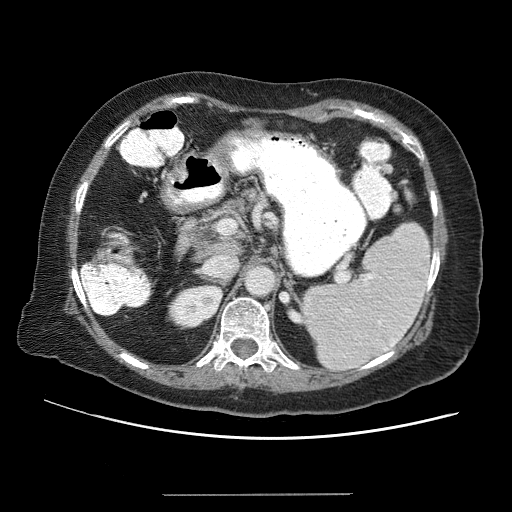
Contrast-enhanced abdominal CT (liver protocol), one axial slice; slice 28 of 65 in the series (ordered by position); reconstruction kernel STANDARD; soft-tissue window (W 400 / L 40 HU); 512 × 512 image matrix. Case-level facts recorded for this patient, not image findings: diagnosis: hepatocellular carcinoma (patient treated with transarterial chemoembolisation; whether this scan precedes or follows treatment is not stated here); TNM stage (as recorded): Stage-IIIB; Child-Pugh class: A; tumour differentiation: moderately differentiated; tumour nodularity: uninodular.
Structures marked on this image (semi-automatic segmentation, software-assisted and operator-edited):
- liver parenchyma outside the tumour (the mass and vessels are separate outlines, so this box may not span the whole liver): bounding box [x1, y1, x2, y2] px = [232, 118, 267, 146]